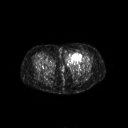
FDG PET of an extremity soft-tissue mass (from a PET/CT study), one axial slice. Slice 35 of 267 in the series (ordered by position). 3.27 mm slice thickness. 128 × 128 image matrix, field of view 700 × 700 mm. Female patient, age 47 years. Case-level facts recorded for this patient, not image findings: histological type: myxofibrosarcoma; grade: intermediate; site of the primary tumour: left thigh.
Outlined on this slice (expert contour drawn on MRI and transferred to this co-registered scan by the dataset authors):
- gross tumour volume including surrounding oedema: bounding box <66,51,83,65> (left, top, right, bottom; pixels)
- gross tumour volume (mass): <66,51,82,62>